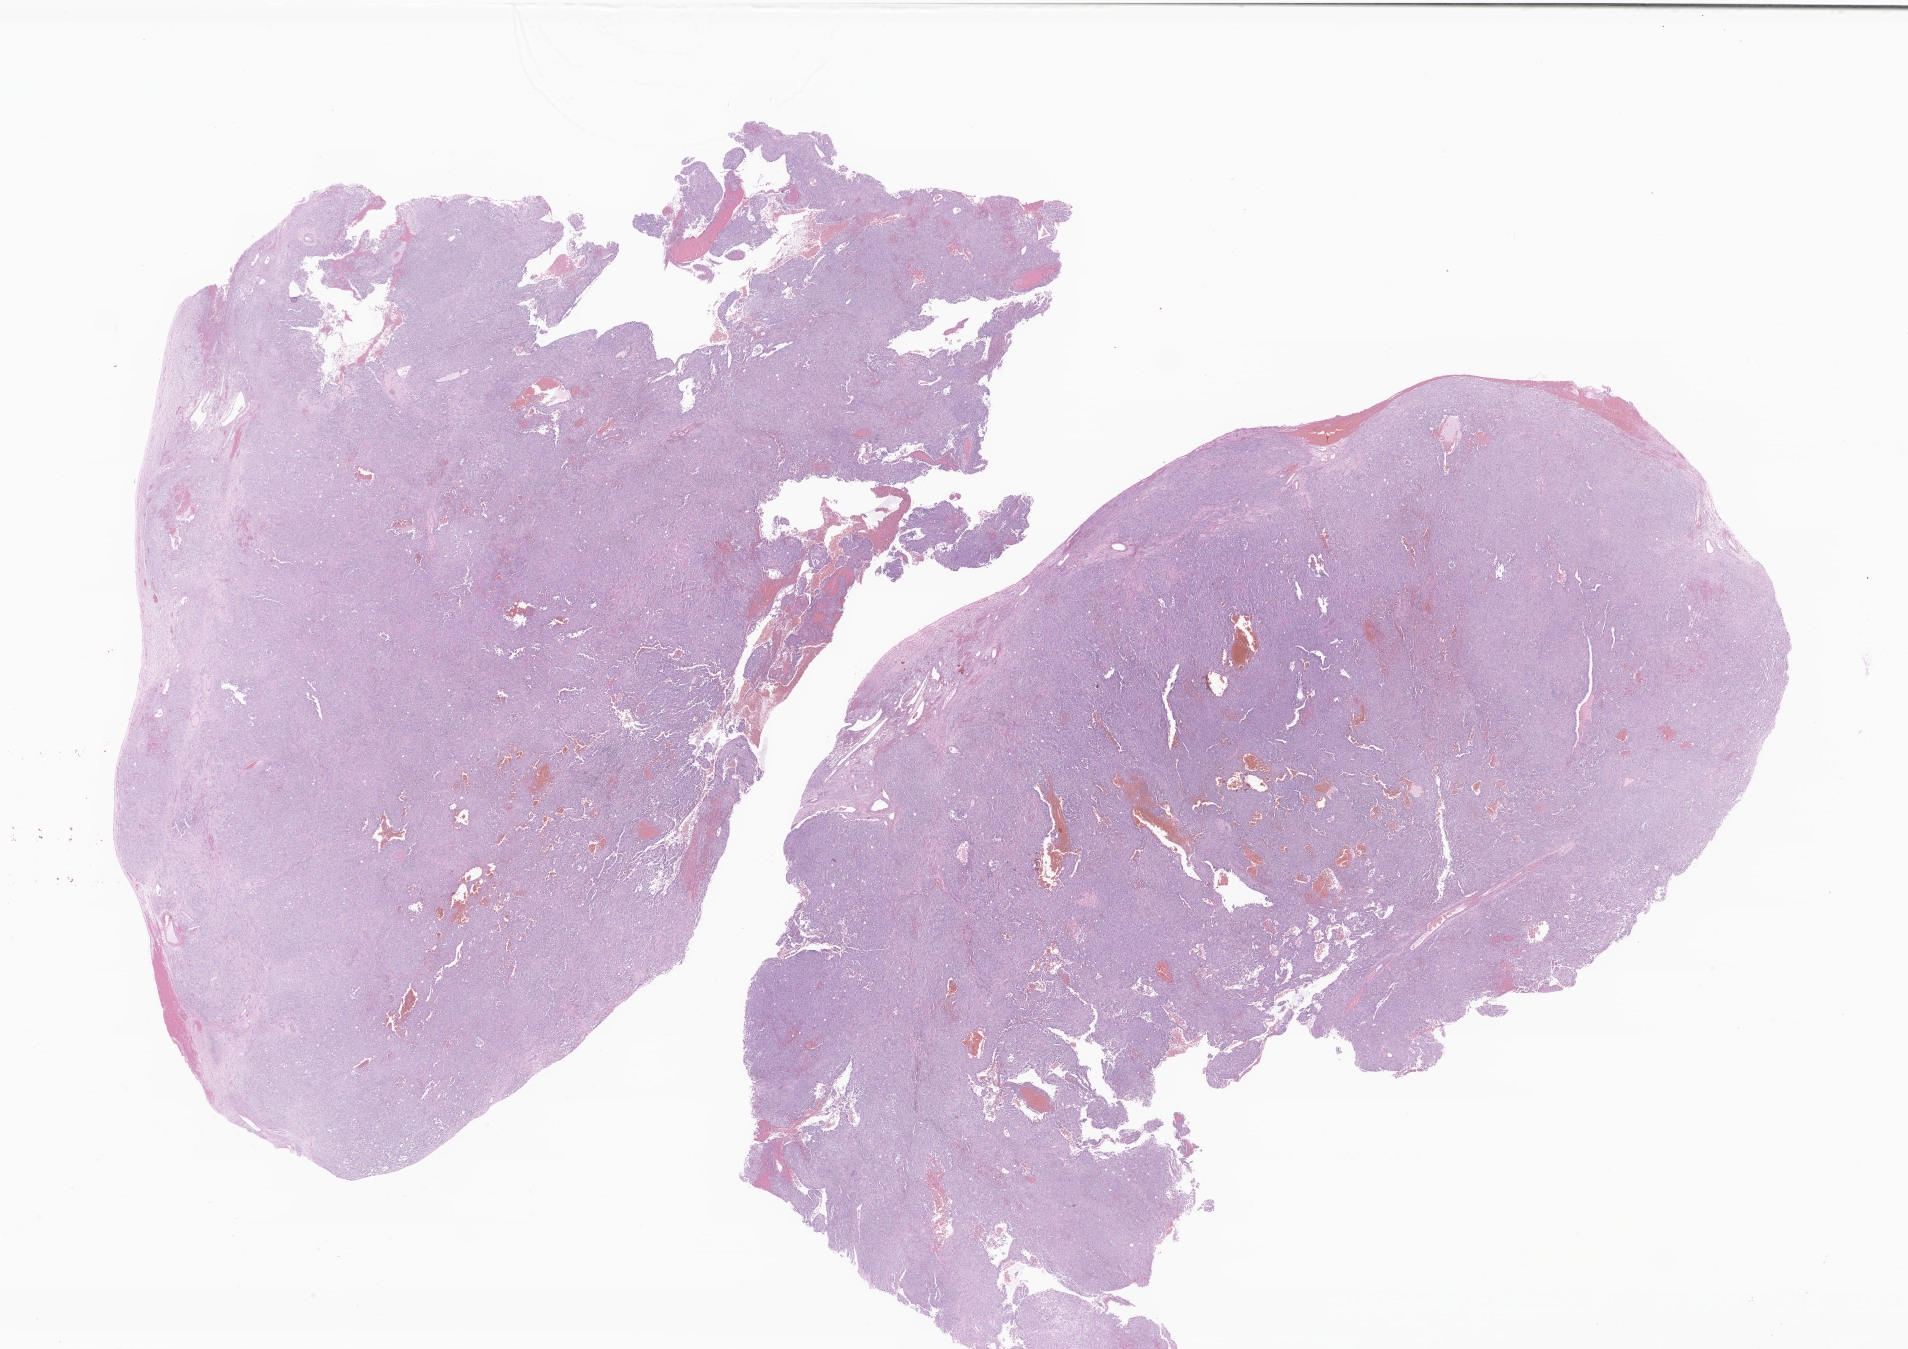
Digitized H&E-stained section of tumor tissue from the ovary, shown as a low-resolution overview of the whole scanned area (about 32.2 x 22.8 mm); FFPE section. Patient female; age 185 months (15 years 5 months).
• diagnosis: Small cell carcinoma, NOS